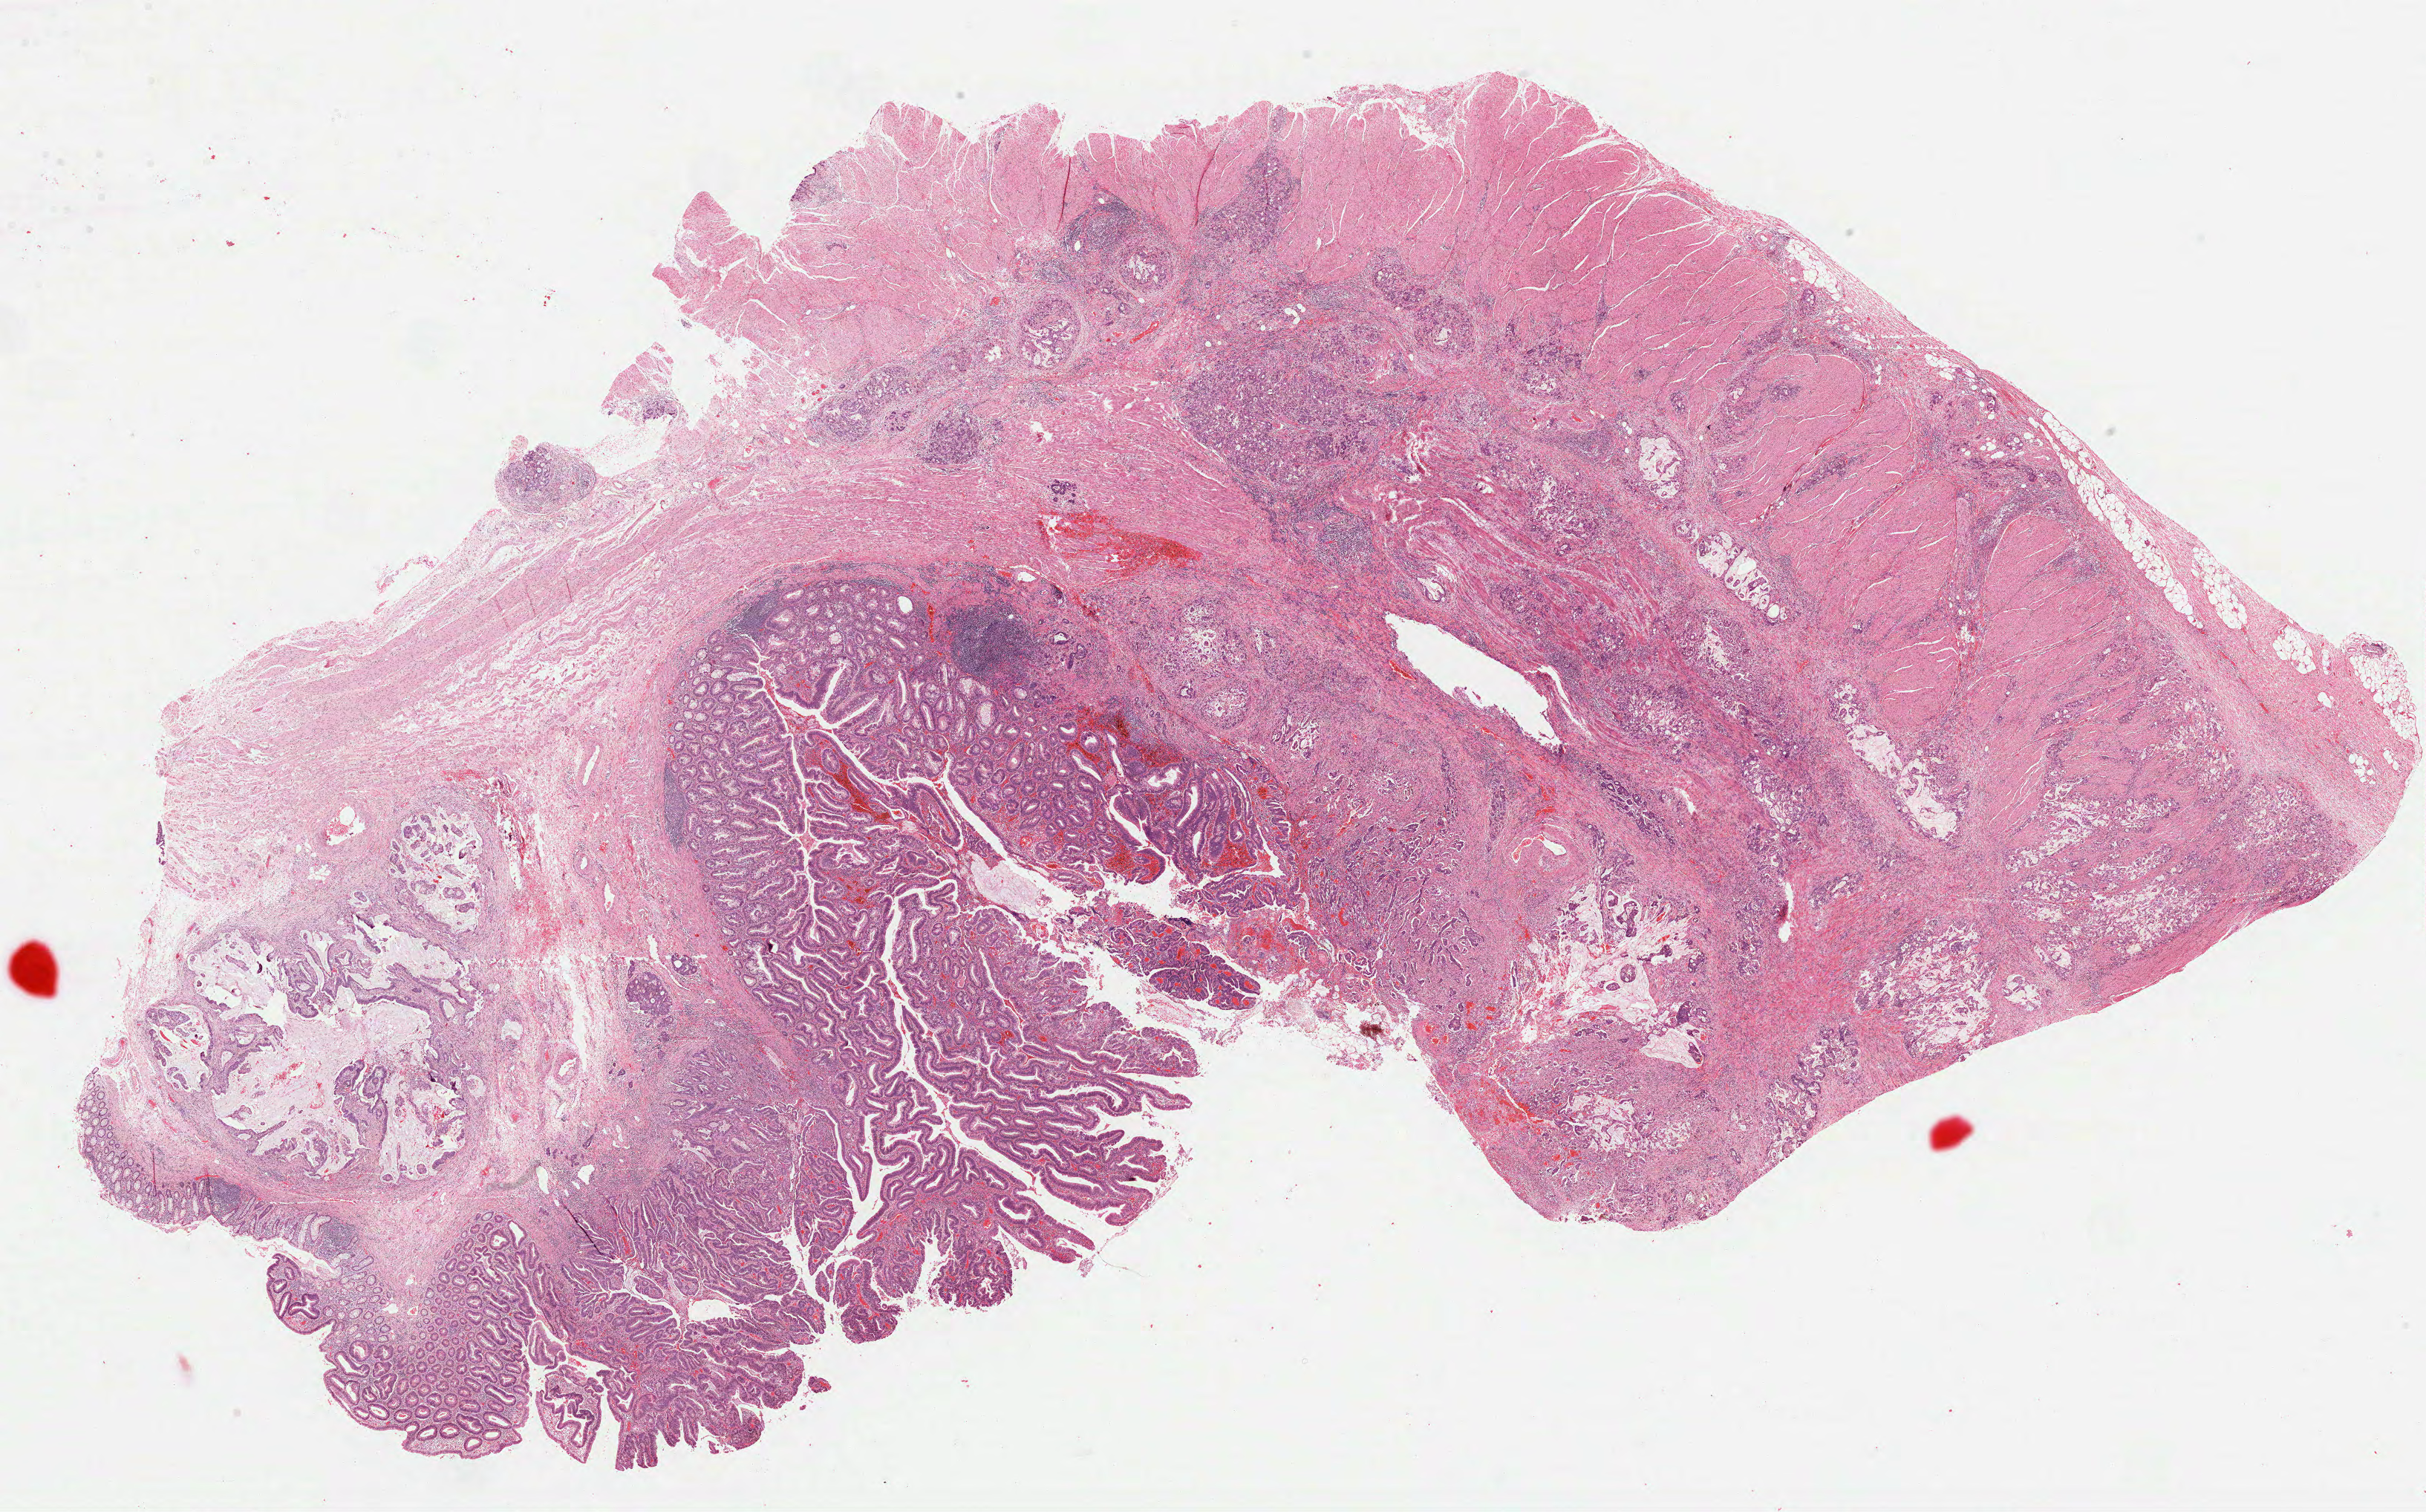
Whole-slide histology image, Hematoxylin and eosin (H&E) stained, shown as a low-resolution overview of the whole scanned area (about 26.3 x 16.4 mm), formalin-fixed paraffin-embedded (FFPE) diagnostic section, sample: primary tumour, rectum. Female patient; age at initial diagnosis 77 years.
- lymph nodes positive (case pathology): 4 of 4 examined
- diagnosis: Adenocarcinoma, NOS (rectosigmoid junction)
- AJCC pathologic stage: IIIC (7th edition)